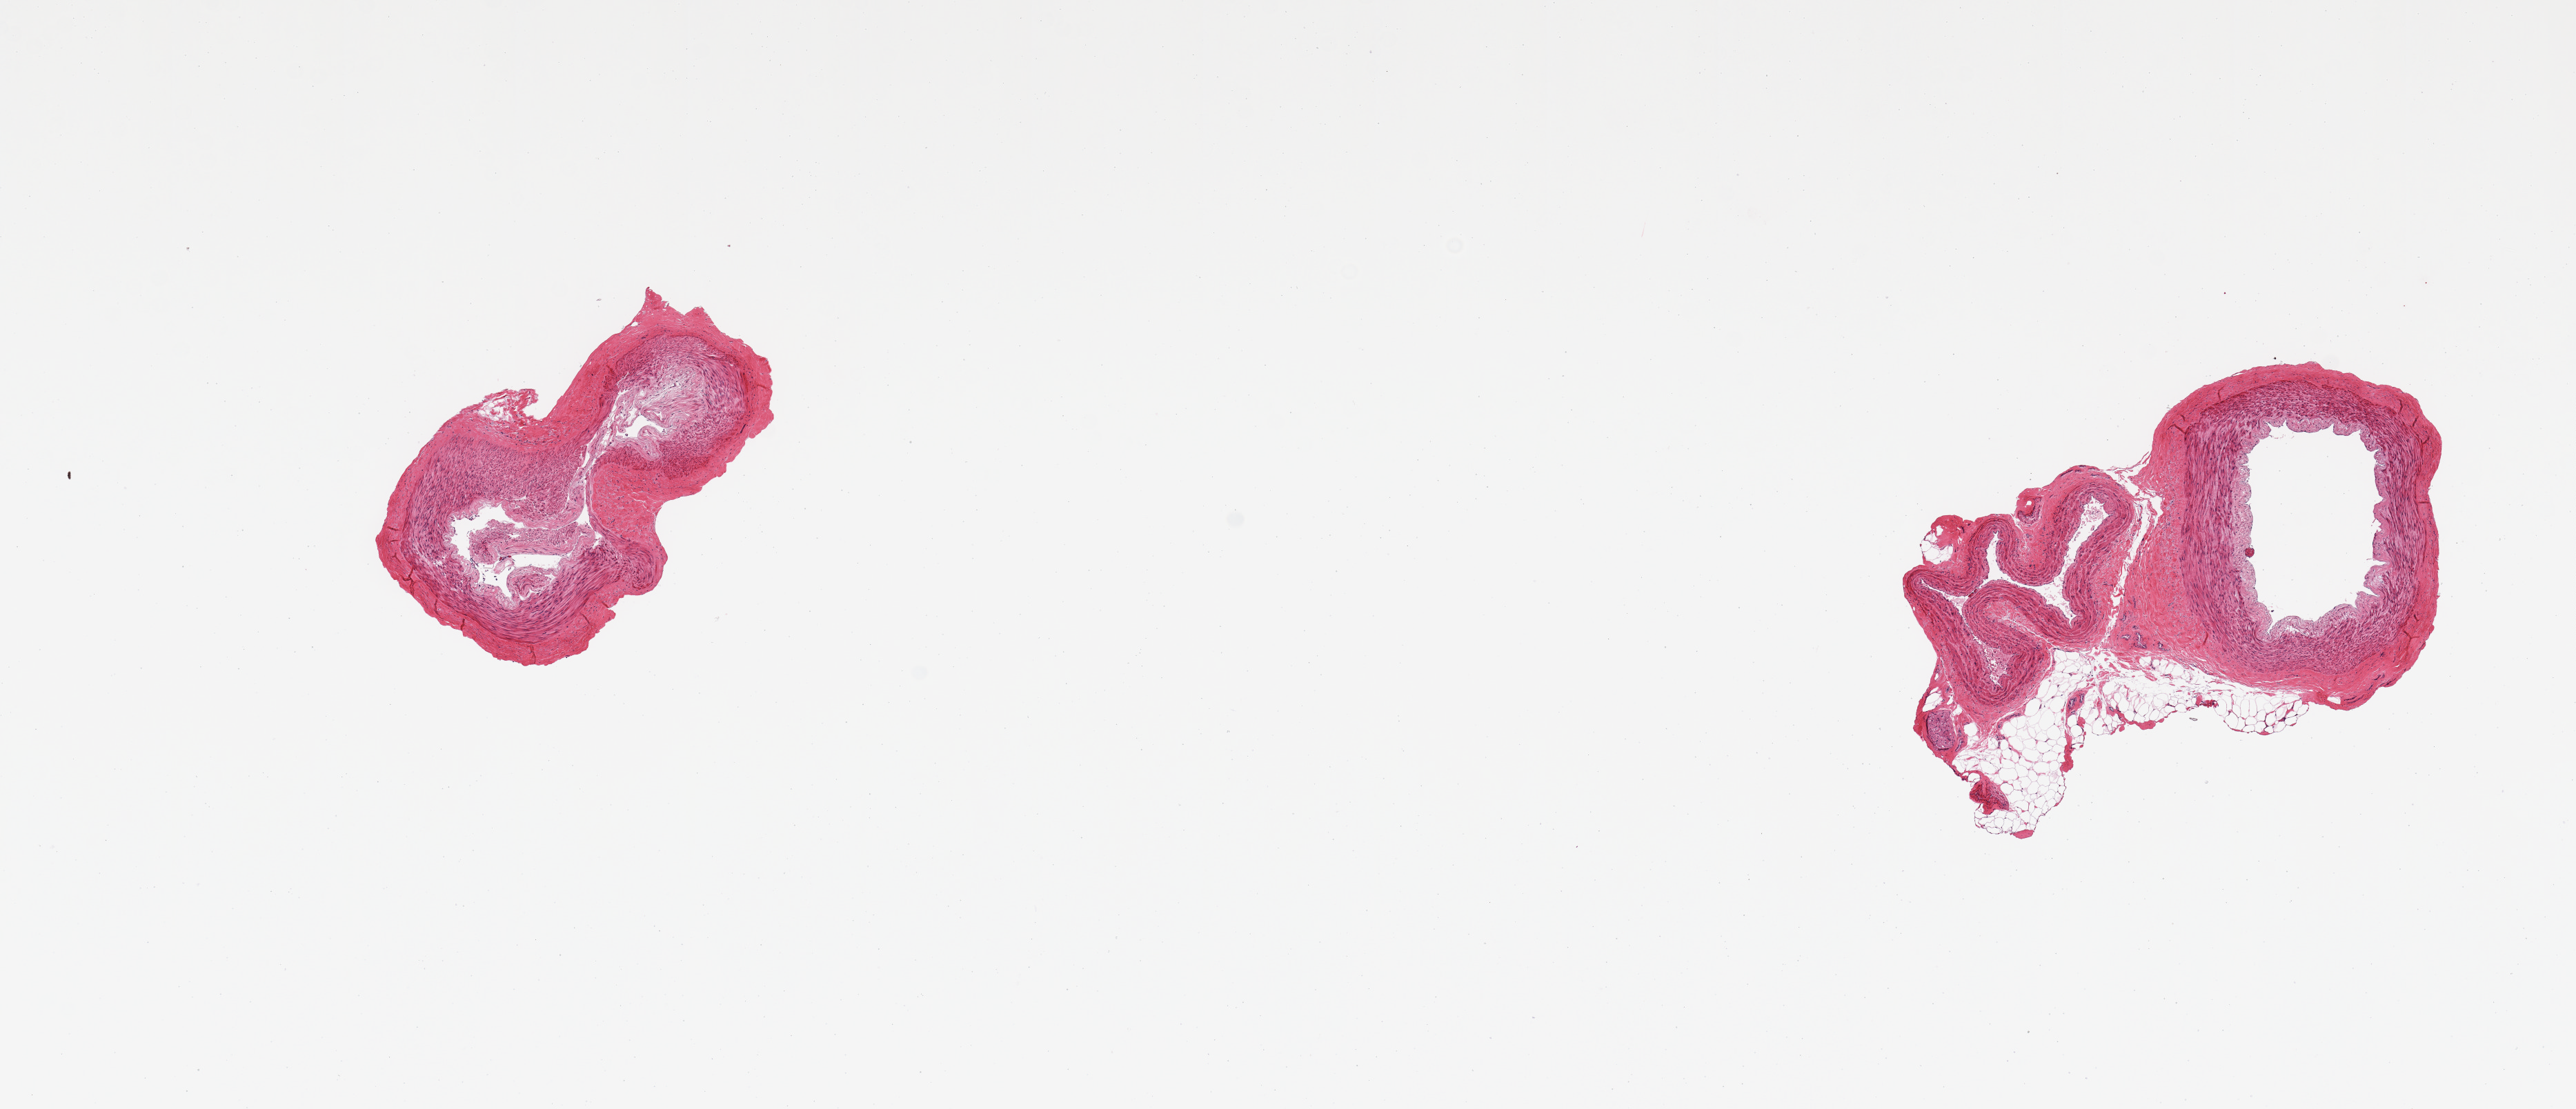
Whole-slide image, hematoxylin and eosin (H&E) stain, brightfield, shown as a low-resolution overview of the whole scanned area (about 14.8 x 6.4 mm). PAXgene-fixed, paraffin-embedded tissue. Section of tibial artery (target tissue). Tissue donor sample. Donor: female.
• reviewer comment on this tissue sample: 2 pieces; 1 piece is well trimmed, 2nd has 40% attachment of fat/vein/nerve